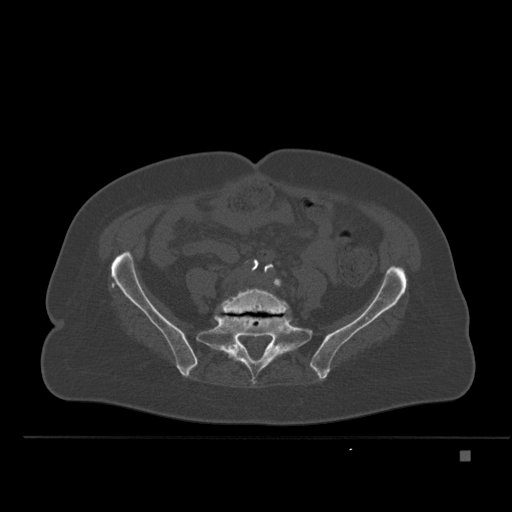
CT including the spine, one axial slice. Position 152 of 477 along the scan axis. Bone window (W 1800 / L 400 HU). 512 × 512 image matrix, field of view 422 × 422 mm. Female patient, age 74 years. From the clinical record (not read from this slice): primary cancer: colon.
Structures marked on this image (semi-automatically segmented with operator editing):
- L5 vertebra: bounding box (x1, y1, x2, y2) in pixels: (217, 278, 290, 353)